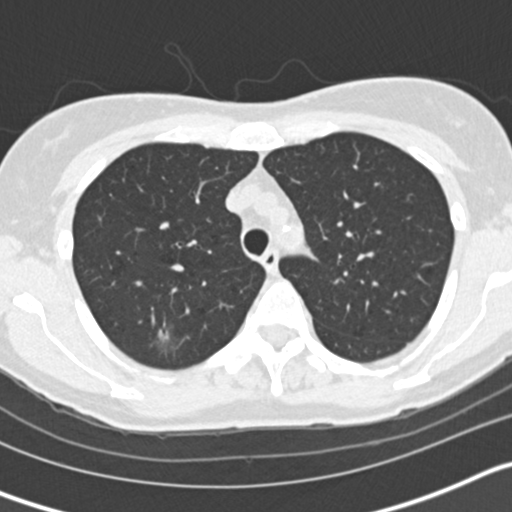
Low-dose screening chest CT, one axial slice. Lung window (W 1500 / L -600 HU). 2 mm slice thickness. 512 × 512 image matrix, field of view 300 × 300 mm.
Structures marked on this image (outlined manually by an expert reader):
- lesion 1 (tumor, upper lobe of right lung): bounding box (x1, y1, x2, y2) in pixels: (158, 324, 169, 341)